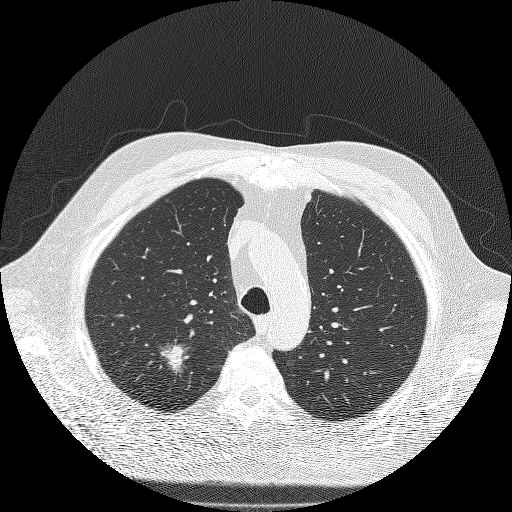
Low-dose screening chest CT, one axial slice; slice 147 of 180 in the series (ordered by position); reconstruction kernel FC51; lung window (W 1500 / L -600 HU); 2 mm slice thickness; 512 × 512 image matrix, field of view 385 × 385 mm.
Structures marked on this image (outlined manually by an expert reader):
- lesion 1 (tumor, upper lobe of right lung): bounding box [x1, y1, x2, y2] px = [160, 345, 189, 372]